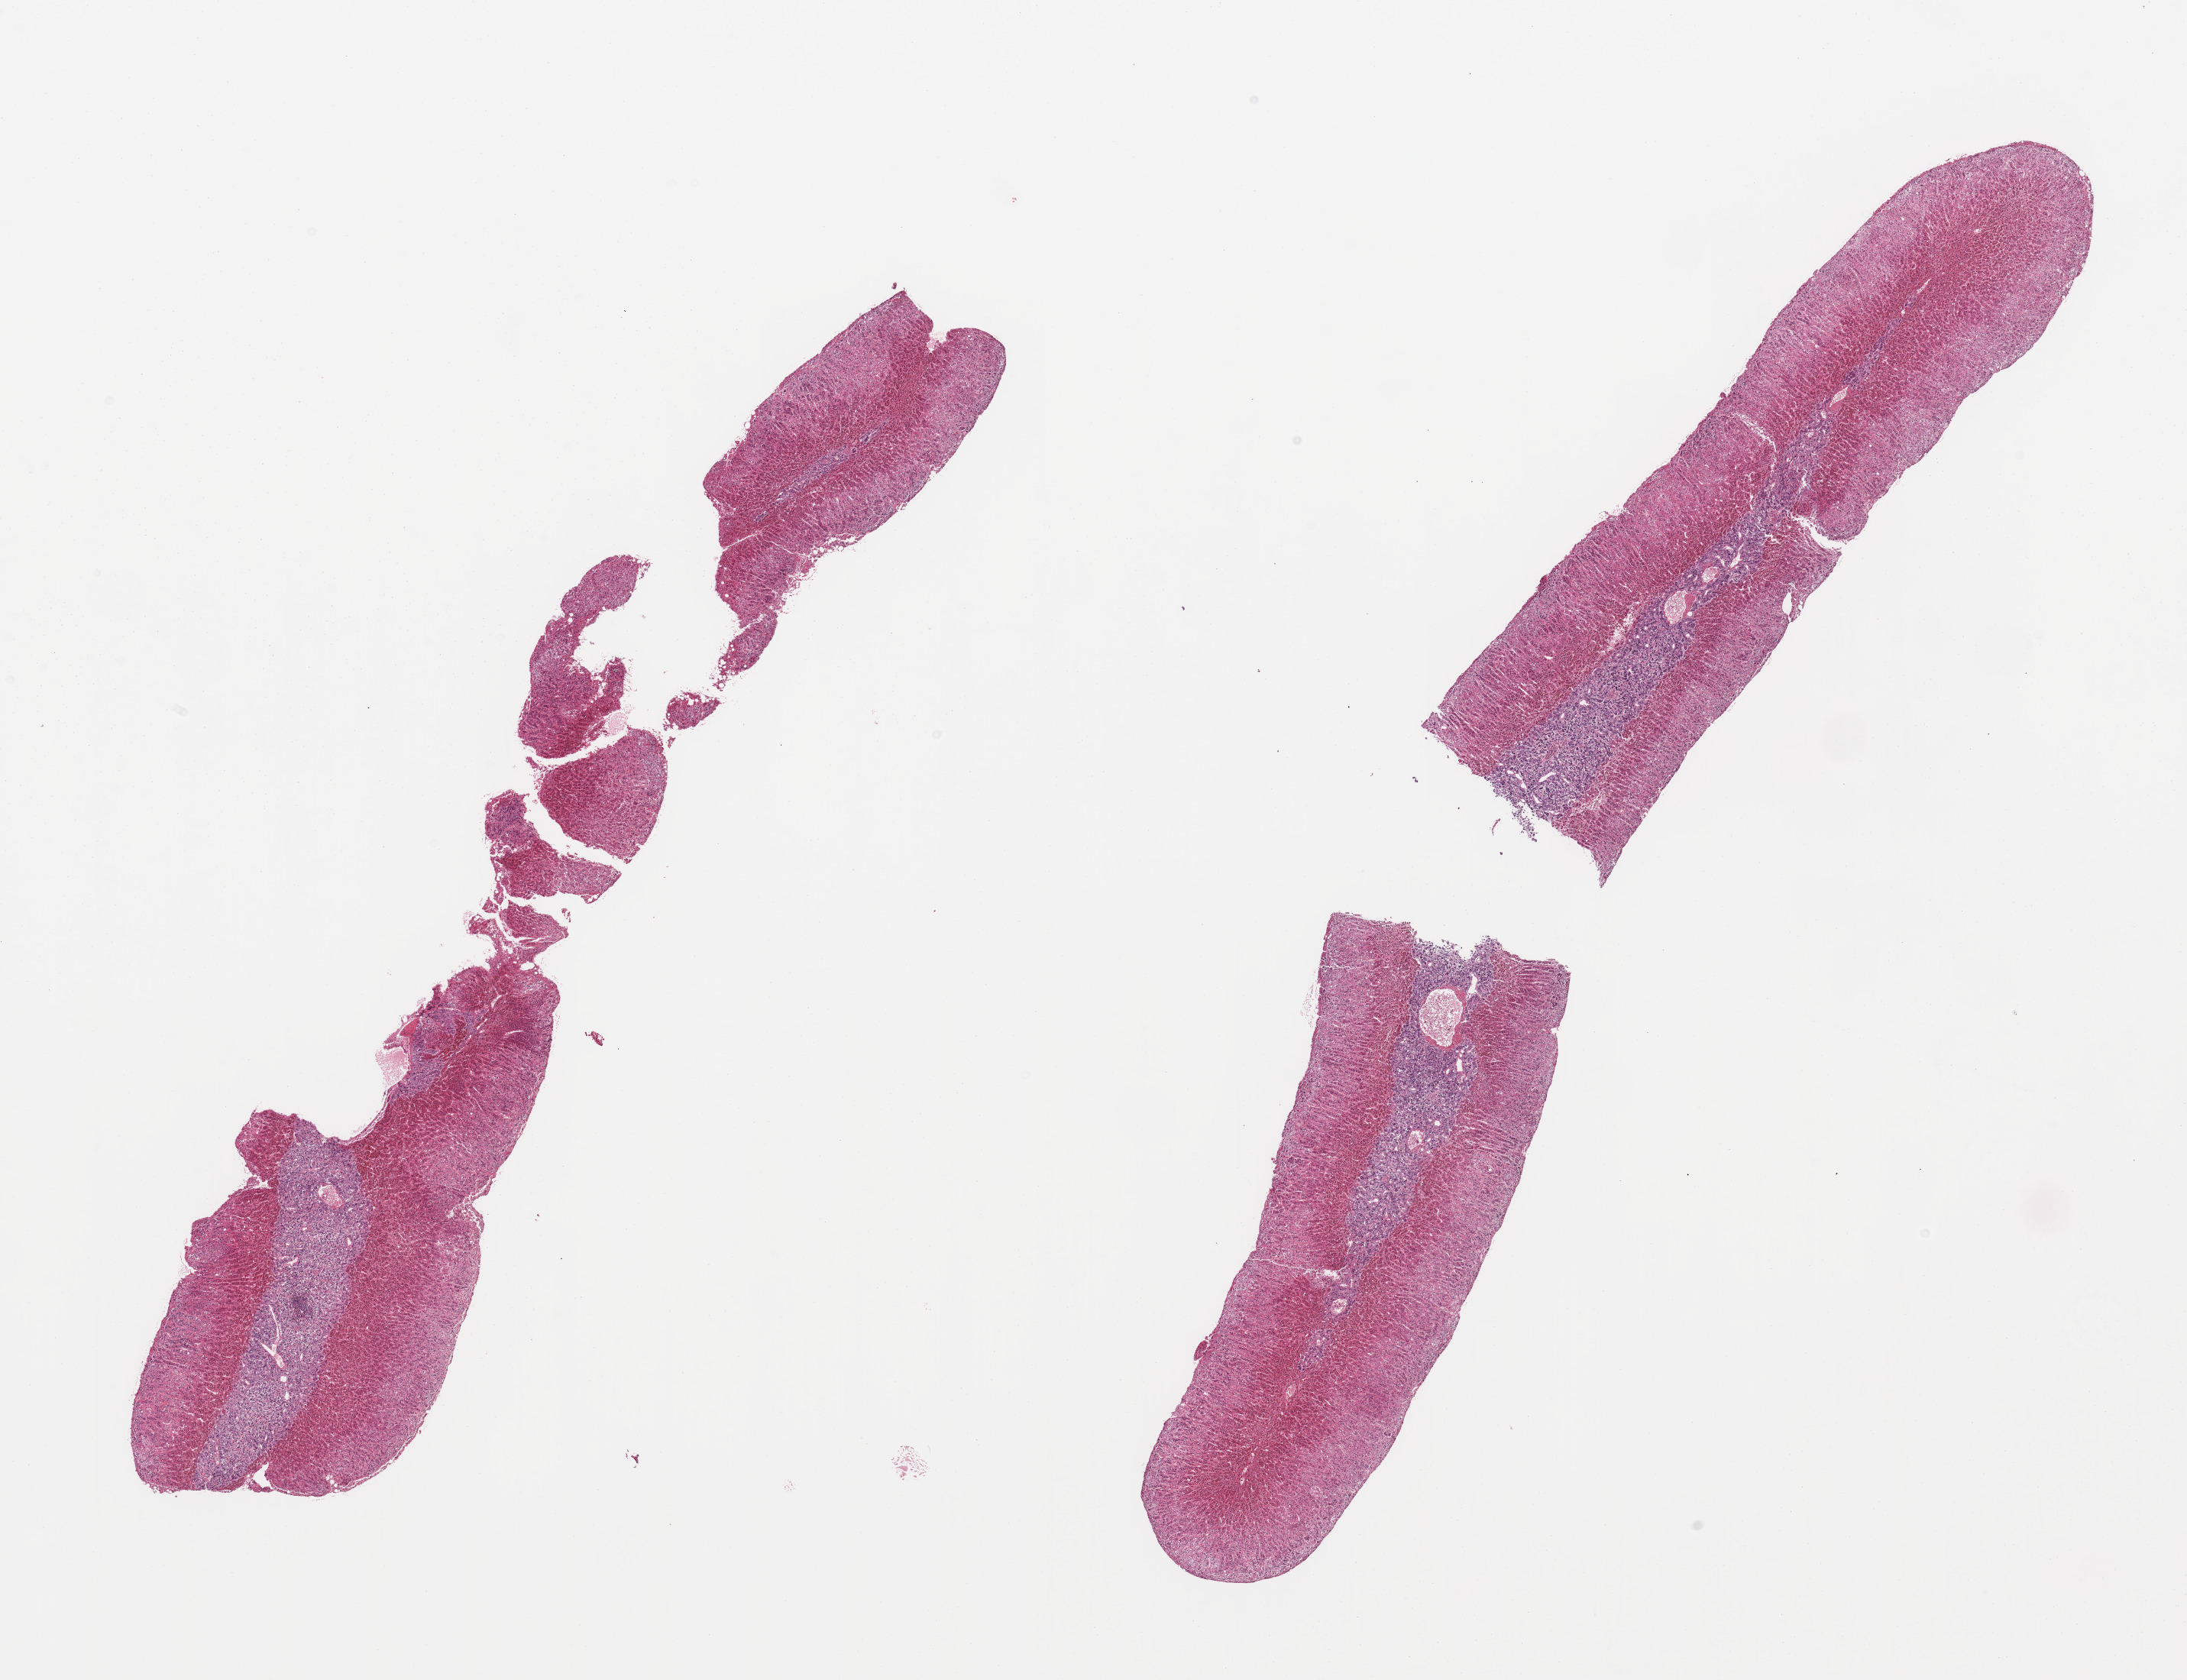
H&E whole-slide image, brightfield, shown as a low-resolution overview of the whole scanned area (about 22.6 x 17.4 mm), PAXgene-fixed, paraffin-embedded tissue, target tissue: adrenal gland, donor tissue sample. Donor sex: male.
* reviewer comment on this tissue sample: 2 pieces (fragmented)--well preserved foci of medulla up to ~10x1mm; valuable specimen